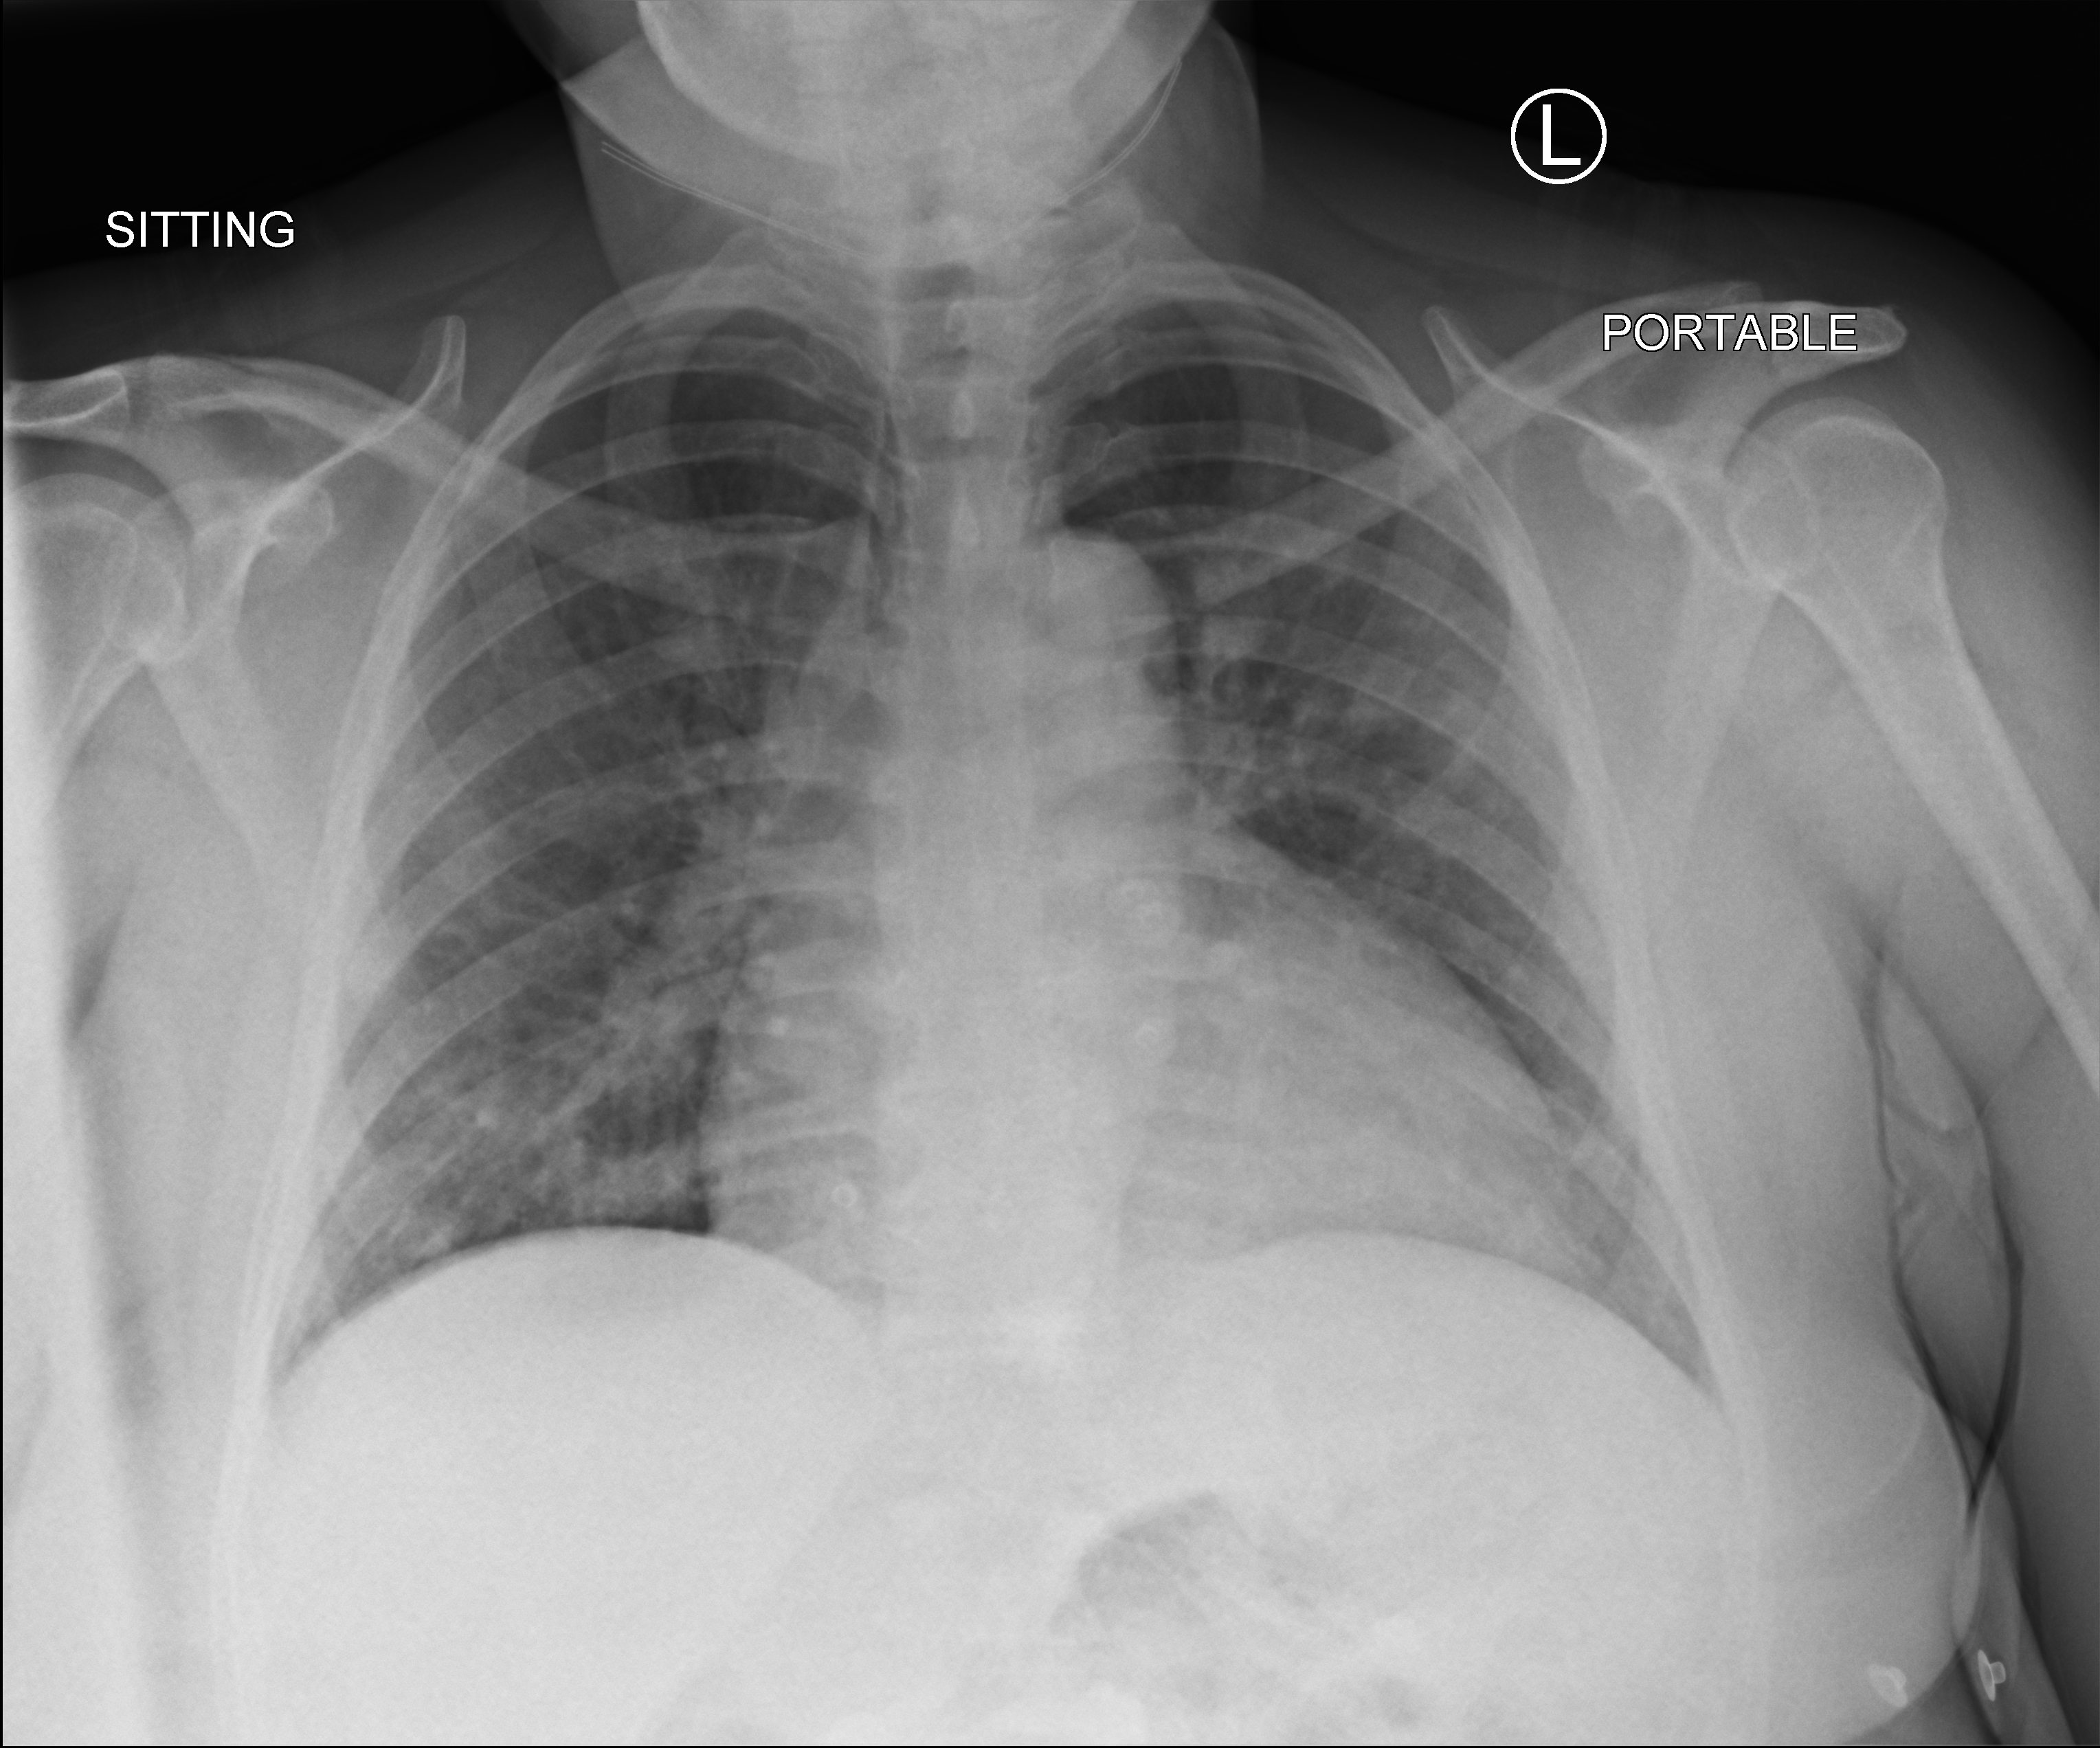
Bedside chest radiograph (computed radiography); anteroposterior (AP) projection. Female patient hospitalised with COVID-19, age 18–59 years.
Hospital-stay facts (about this admission, not read from this image; timing relative to this image not recorded): admitted to intensive care during this hospital stay: no; mechanically ventilated during this hospital stay: no.